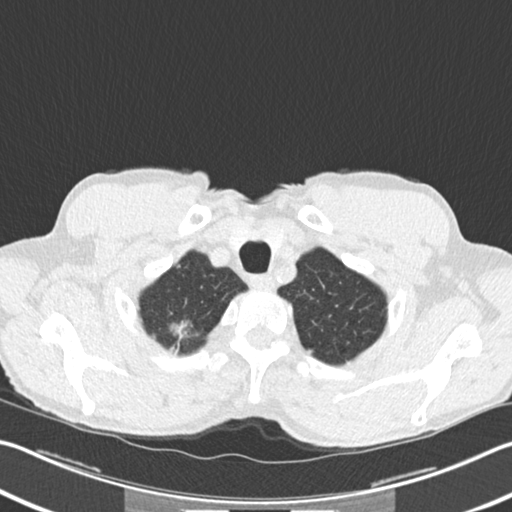
Axial slice from a low-dose chest CT screening exam, second annual screen, lung window (W 1500 / L -600 HU), 2 mm slice thickness, standard (soft-tissue) reconstruction kernel (B30f). Male participant, aged 62 years at enrolment. Former smoker at enrolment.
Lesion marked by an expert reader, bounding box (x1, y1, x2, y2) in pixels: (159, 309, 205, 351). The screening reader recorded 2 non-calcified nodules or masses ≥4 mm on this exam (right upper lobe, right upper lobe); which of them this box marks is not recorded. Lung cancer was diagnosed 5 days after this screen: bronchiolo-alveolar adenocarcinoma, NOS, right upper lobe, well differentiated (G1), stage IA (AJCC 6th edition), 15 mm at pathology.